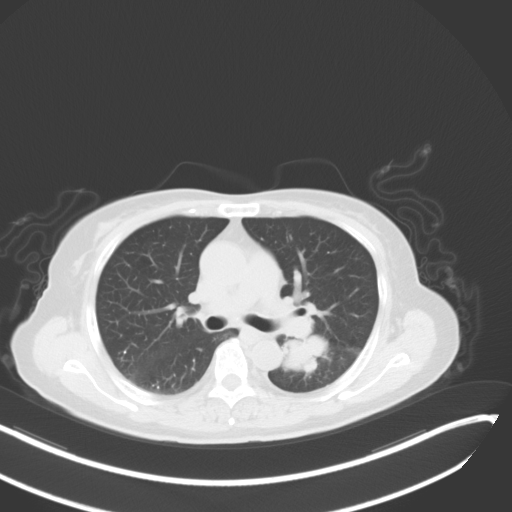
Chest CT, one axial slice. Position 24 of 48 along the scan axis. Reconstruction kernel B31f. Lung window (W 1500 / L -600 HU). 512 × 512 image matrix, field of view 400 × 400 mm. Patient: female, 64 years. From the clinical record (not read from this slice): clinical TNM (as recorded): T3 N1 M1.
Outlined on this slice (rectangle marked by the reading radiologist):
- lung tumour (recorded histology: small cell carcinoma): bounding box [x1, y1, x2, y2] px = [274, 319, 338, 379]